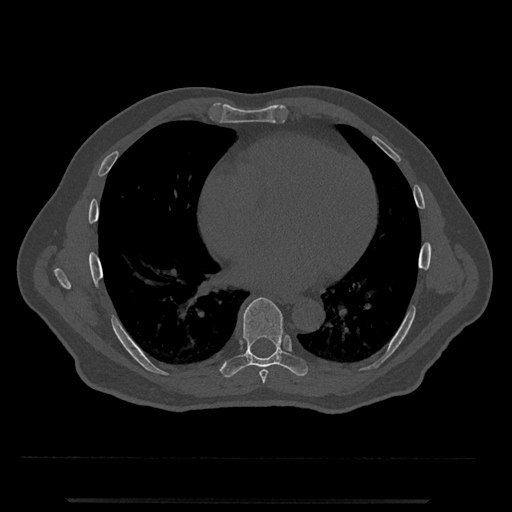
CT including the spine, one axial slice. Position 638 of 797 along the scan axis. 120 kVp. Bone window (W 1800 / L 400 HU). 512 × 512 image matrix, field of view 419 × 419 mm. Patient: male, 63 years. Case-level facts recorded for this patient, not image findings: primary cancer: prostate.
Outlined on this slice (semi-automatic segmentation, software-assisted and operator-edited):
- T7 vertebra: bounding box (x1, y1, x2, y2) in pixels: (259, 369, 268, 384)
- T8 vertebra: (220, 297, 308, 378)